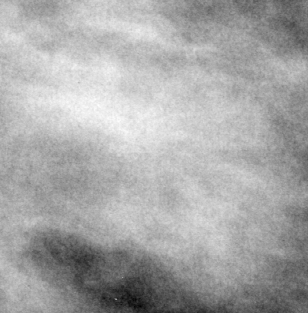
Cropped region of a digitized screen-film mammogram centred on a radiologist-marked abnormality, left breast, MLO view.
- Mass, shape lobulated, margins circumscribed / ill defined; BI-RADS assessment category 3; pathology (as recorded): malignant.